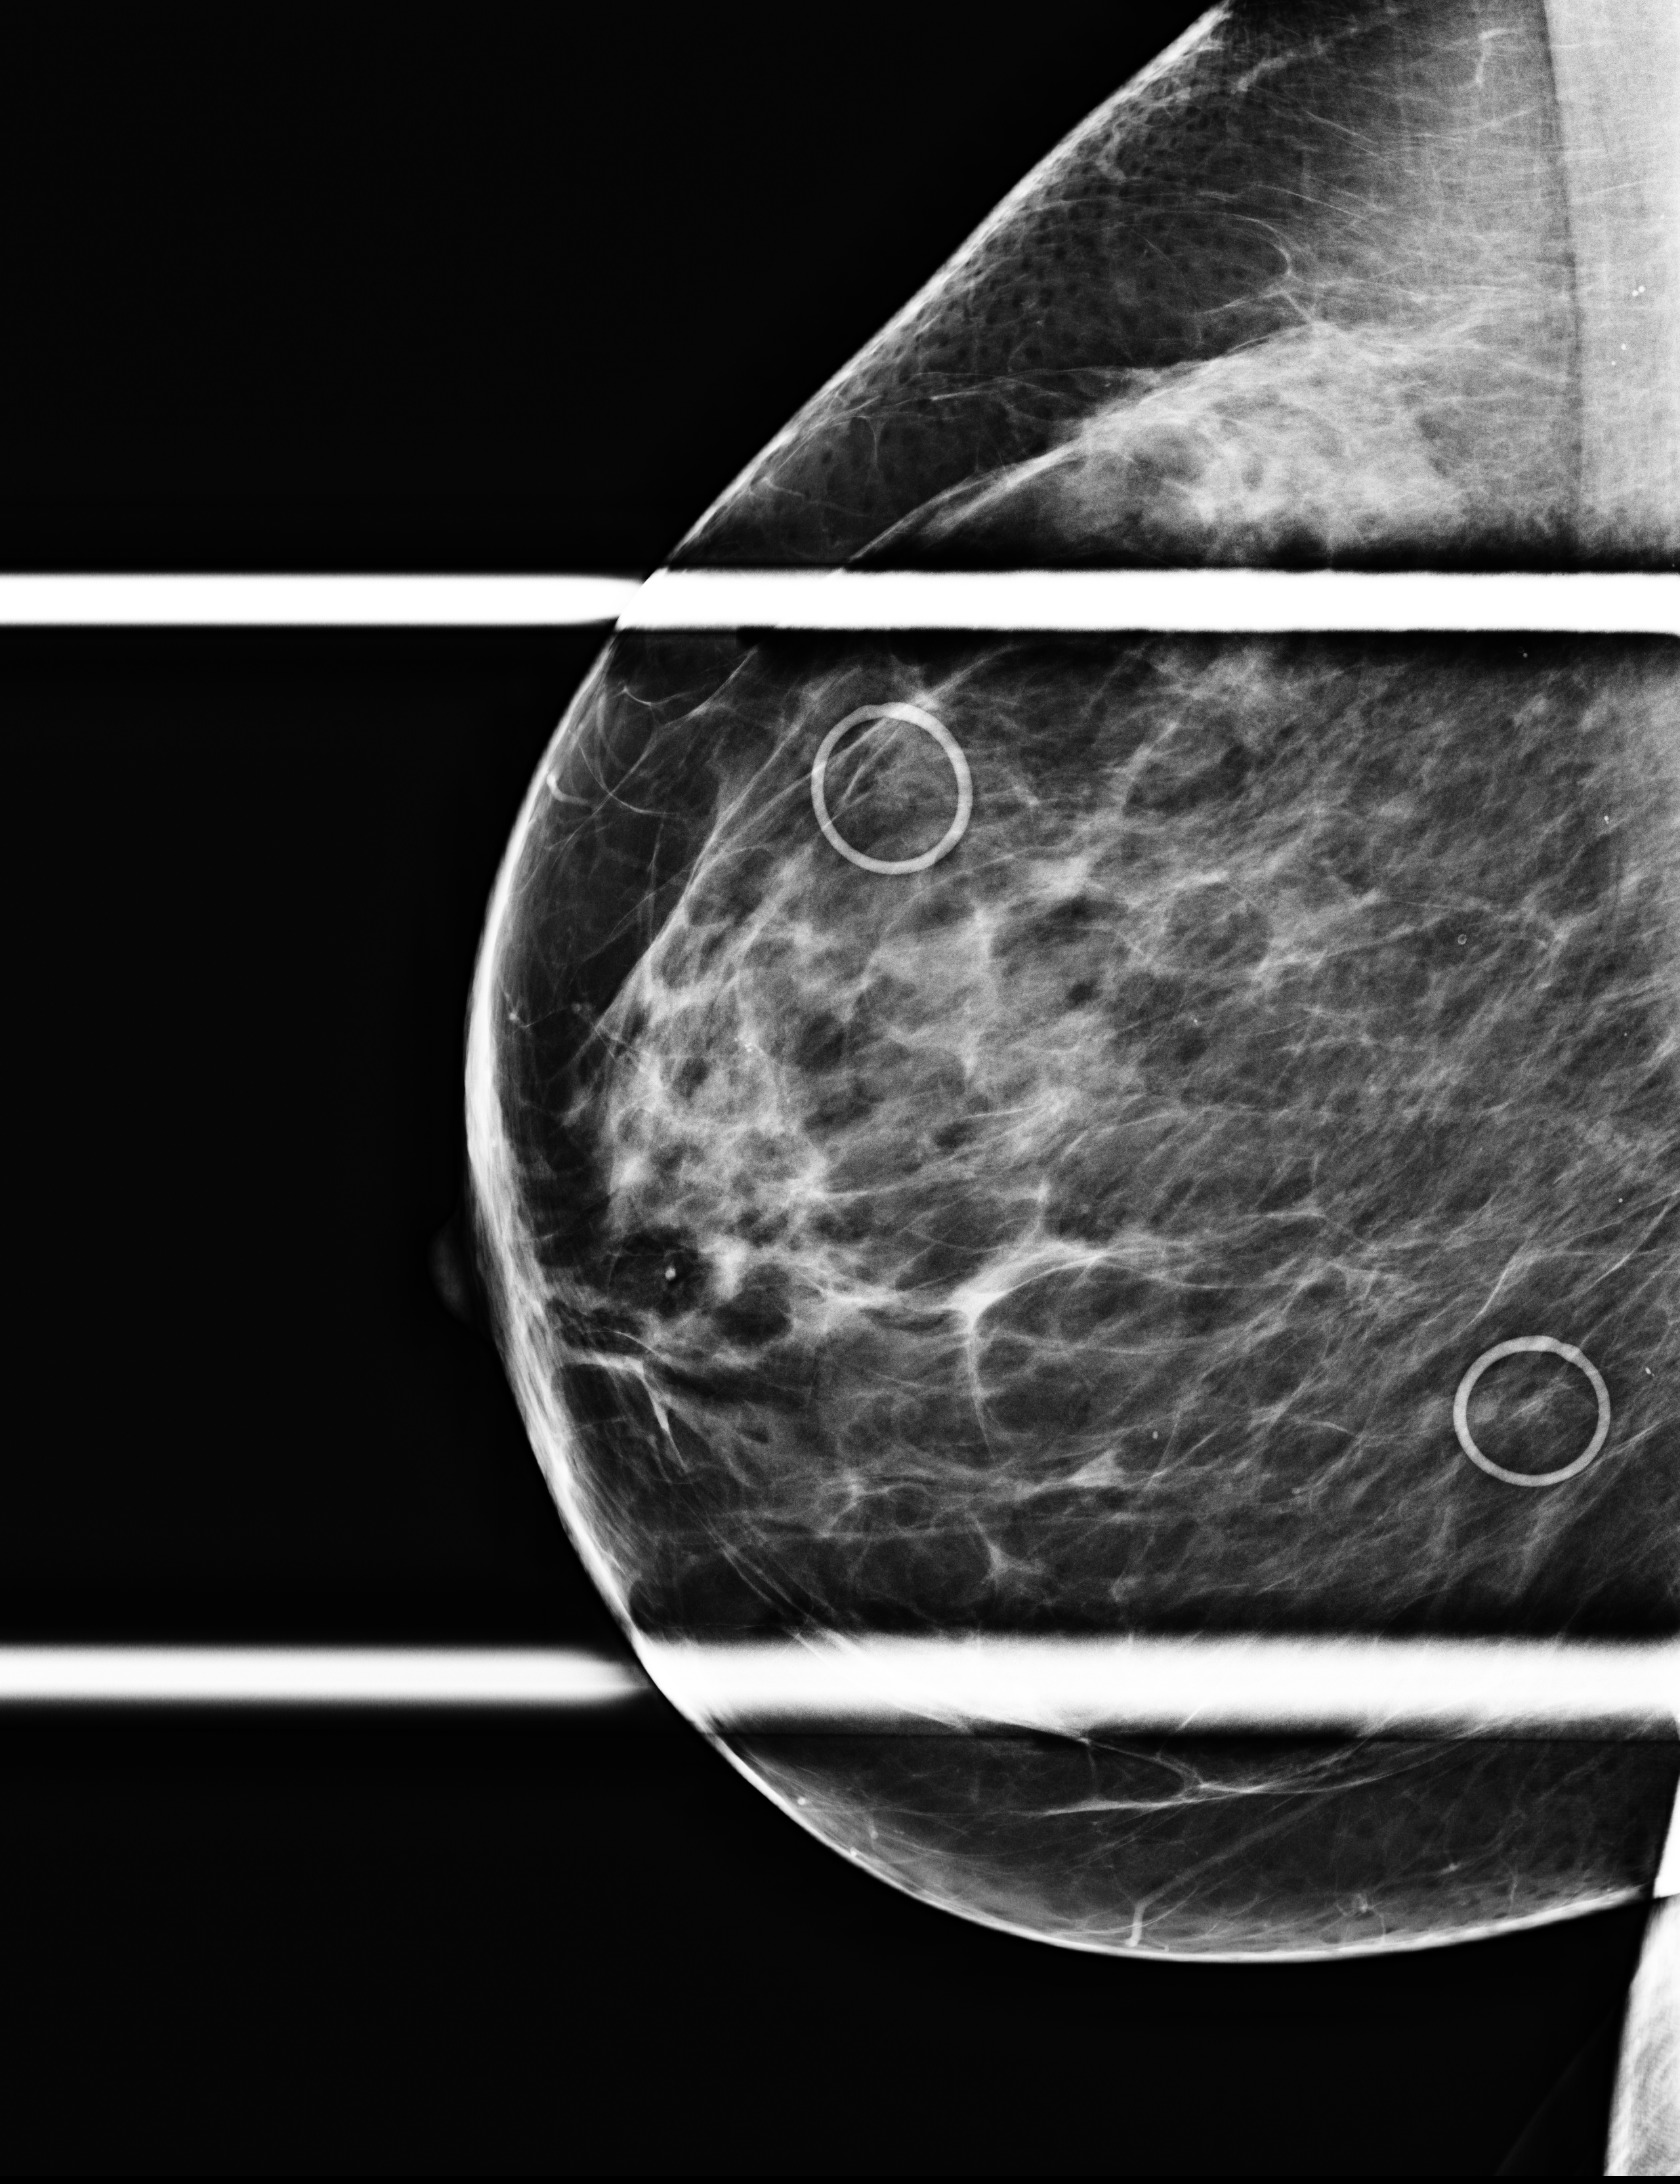
Additional (diagnostic) view. Female patient, age 60 years.
Image type: full-field digital mammogram. Breast: right. Projection: mediolateral oblique (MLO) view, spot compression.